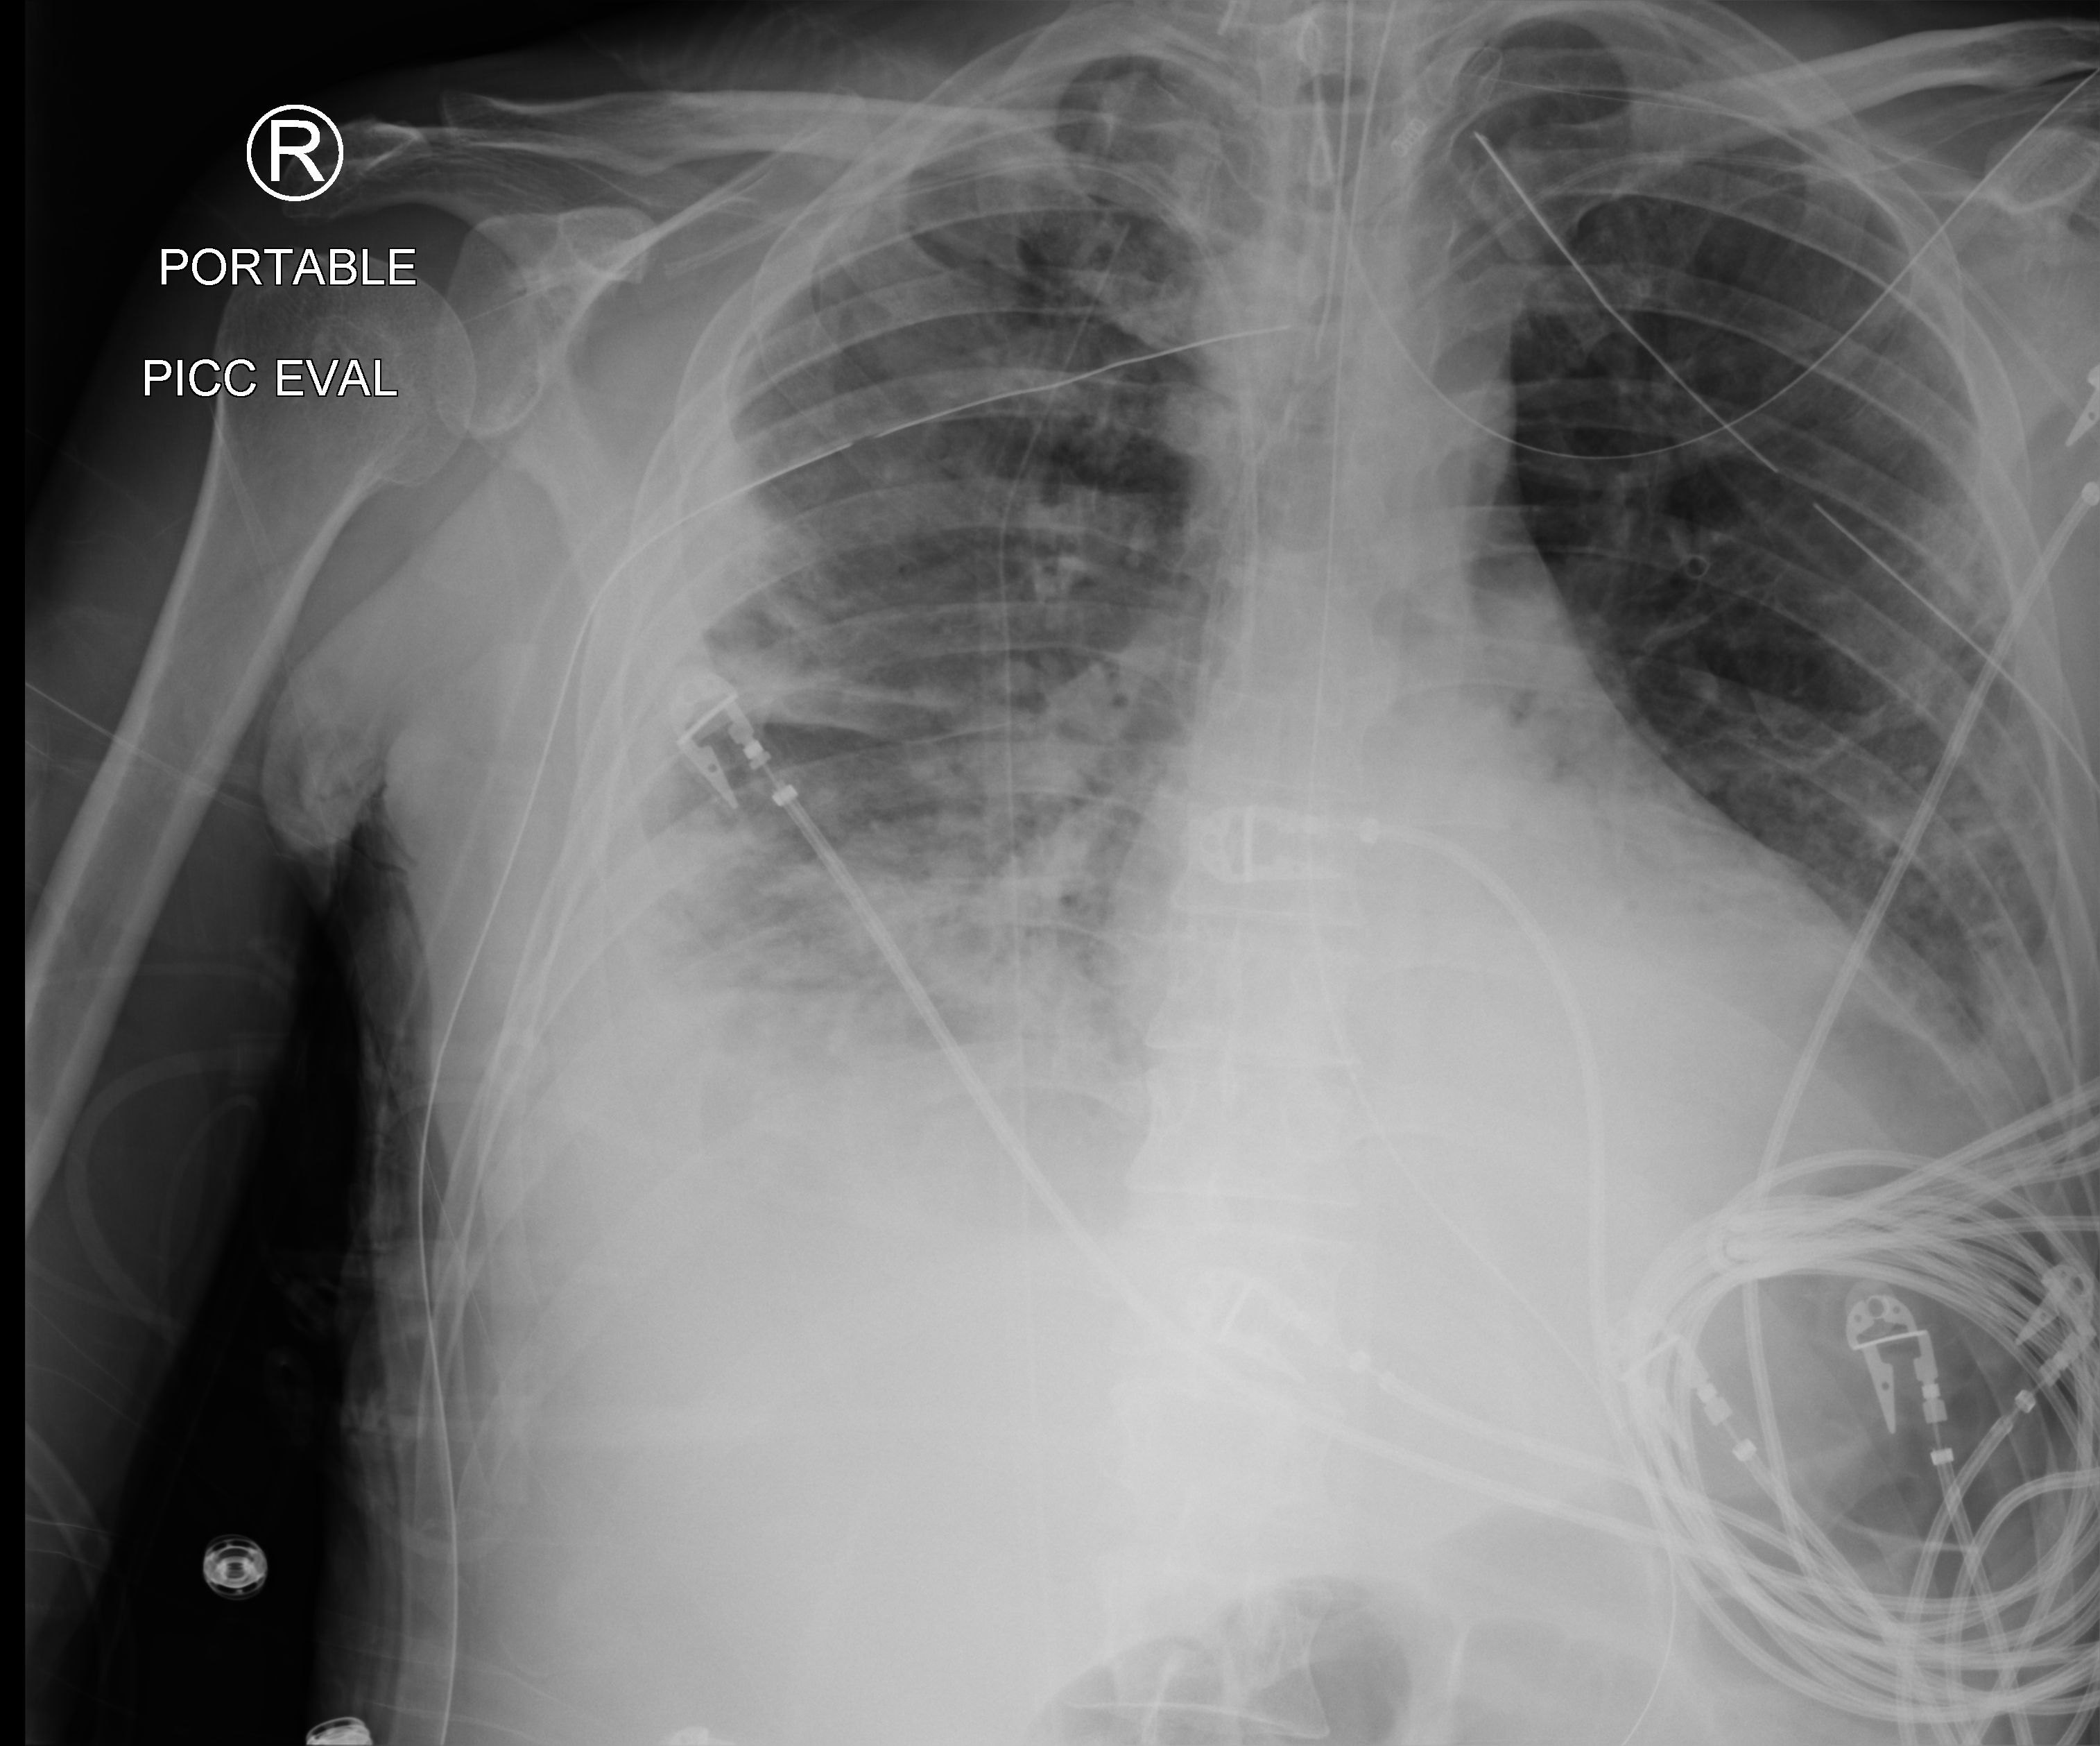
Chest X-ray (portable). Male patient hospitalised with COVID-19, age 18–59 years.
Admission-level facts for this patient (not findings on this image; timing relative to this image not recorded): smoking status (admission record): never; mechanically ventilated during this hospital stay: yes.